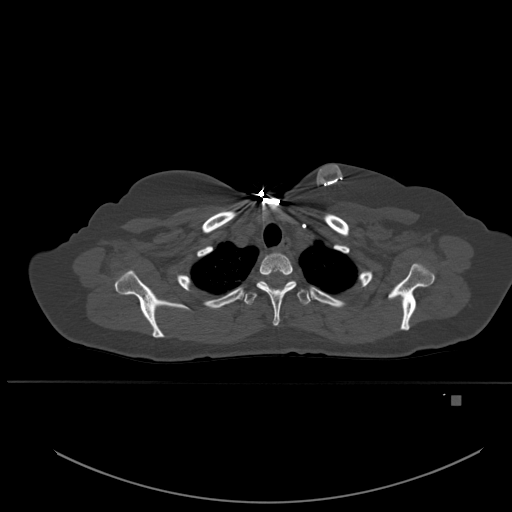
CT including the spine, one axial slice; position 414 of 651 along the scan axis; bone window (W 1800 / L 400 HU); 1.5 mm slice thickness; 512 × 512 image matrix, field of view 443 × 443 mm. Female patient, age 49 years. From the clinical record (not read from this slice): primary cancer: breast; vertebrae with lytic lesions (as recorded): L3, T12, L4.
Annotated regions visible in this slice (semi-automatically segmented with operator editing):
- T1 vertebra: bounding box [x1, y1, x2, y2] px = [256, 252, 296, 326]
- T2 vertebra: [244, 281, 311, 305]